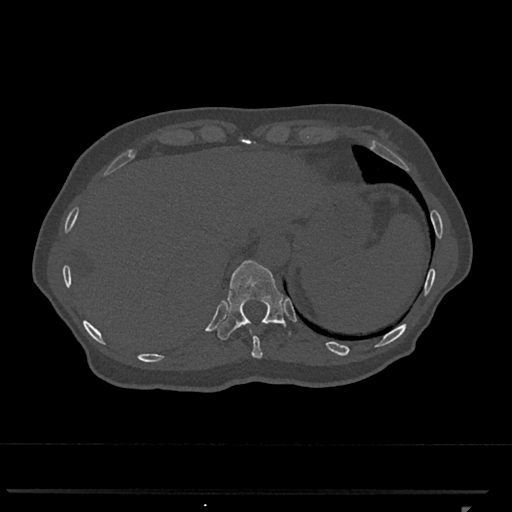
CT including the spine, one axial slice. Position 534 of 793 along the scan axis. 120 kVp. Bone window (W 1800 / L 400 HU). 0.5 mm slice thickness. 512 × 512 image matrix, field of view 380 × 380 mm. Patient: female, 62 years. Case-level facts recorded for this patient, not image findings: primary cancer: renal.
Annotated regions visible in this slice (semi-automatic segmentation, software-assisted and operator-edited):
- T10 vertebra: bounding box [x1, y1, x2, y2] px = [249, 330, 263, 359]
- T11 vertebra: [217, 260, 291, 340]